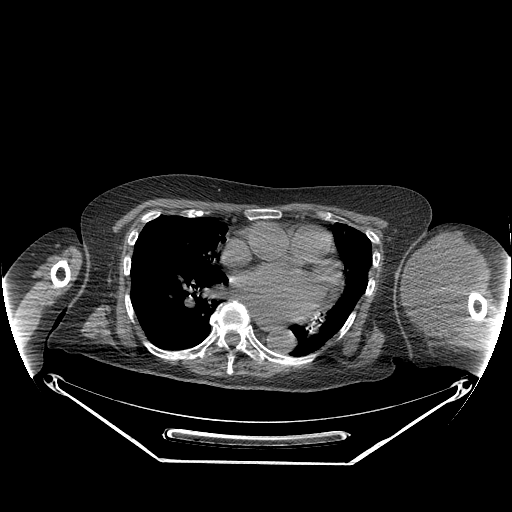
CT of an extremity soft-tissue mass (from a PET/CT study), one axial slice; slice 170 of 267 in the series (ordered by position); reconstruction kernel STANDARD; 140 kVp; soft-tissue window (W 400 / L 40 HU); 3.75 mm slice thickness; 512 × 512 image matrix, field of view 500 × 500 mm. Female patient. From the clinical record (not read from this slice): histological type: pleiomorphic leiomyosarcoma; grade: high; site of the primary tumour: left biceps.
Structures marked on this image (expert contour drawn on MRI and transferred to this co-registered scan by the dataset authors):
- gross tumour volume including surrounding oedema: bounding box [x1, y1, x2, y2] px = [402, 233, 483, 330]
- gross tumour volume (mass): [404, 233, 476, 323]